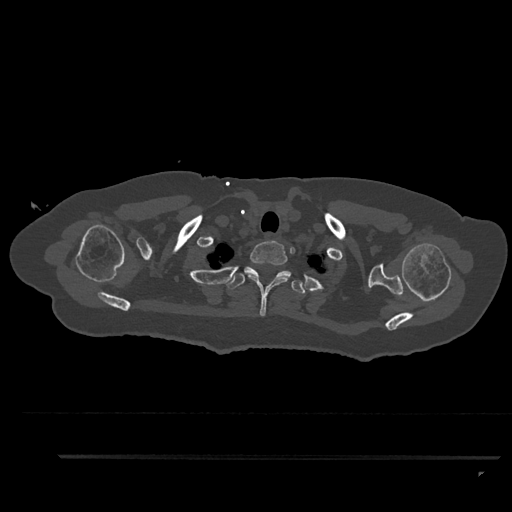
CT including the spine, one axial slice; slice 745 of 797 in the series (ordered by position); bone window (W 1800 / L 400 HU); 0.5 mm slice thickness; 512 × 512 image matrix. Female patient, age 44 years. Case-level facts recorded for this patient, not image findings: primary cancer: renal; vertebrae with lytic lesions (as recorded): L1.
Structures marked on this image (semi-automatic segmentation, software-assisted and operator-edited):
- T1 vertebra: box from (x=247, y=240) to (x=291, y=316) px
- T2 vertebra: (x=226, y=267)–(x=306, y=294)